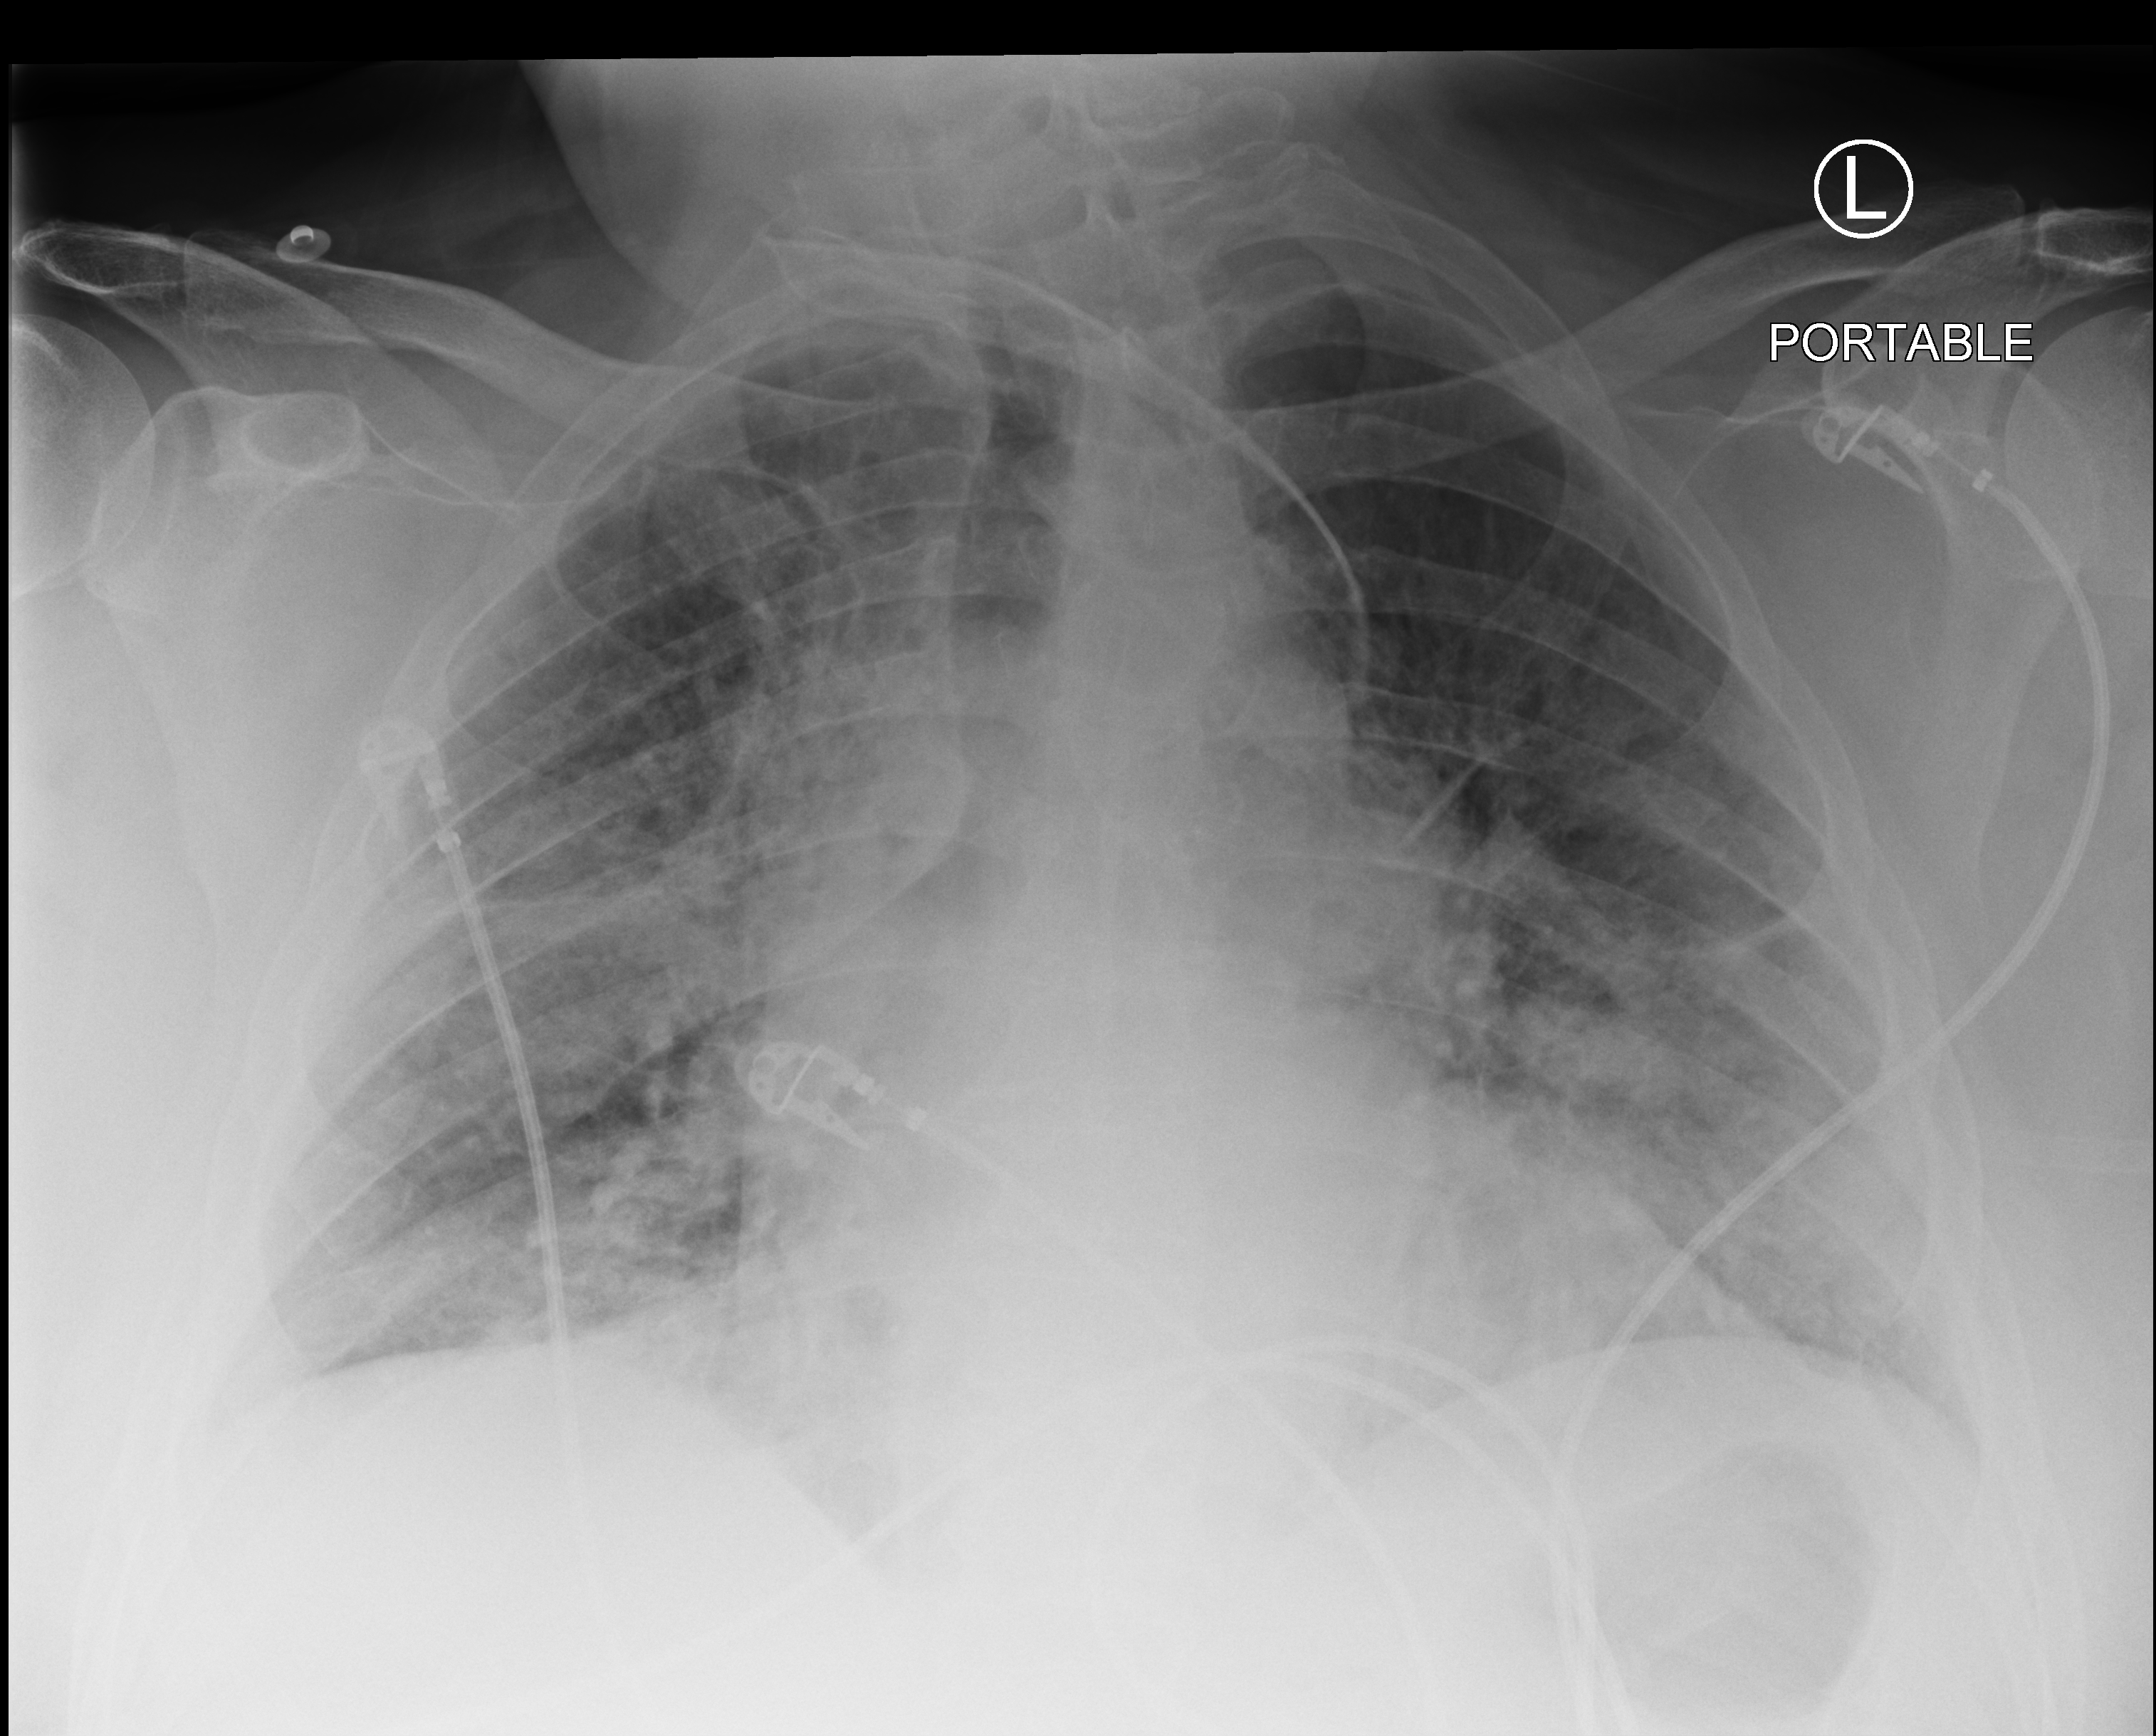
Portable chest radiograph, anteroposterior (AP) projection. Patient hospitalised with COVID-19; male, aged 60–74 years.
From the hospital-stay record, not from the radiograph (when in the stay this image was taken is not recorded):
- admitted to intensive care during this hospital stay: yes